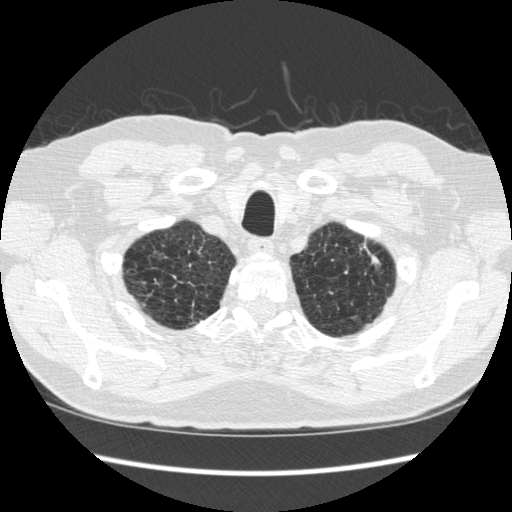
Chest CT (low-dose screening protocol), one axial image. Second screening round (one year after baseline). Lung window (W 1500 / L -600 HU). 1.25 mm slice thickness. Standard (soft-tissue) reconstruction kernel (STANDARD). 120 kVp. 512 × 512 image matrix, field of view 348 × 348 mm. Male participant, aged 70 years at enrolment. Former smoker at enrolment.
• Expert-annotated lung lesion, bounding box <325,233,388,302> (left, top, right, bottom; pixels).
• The screening reader recorded 5 non-calcified nodules or masses ≥4 mm on this exam (right lower lobe, right lower lobe, right lower lobe, left upper lobe, left lower lobe); which of them this box marks is not recorded.
• Official screen result: positive, change unspecified: nodule(s) >= 4 mm or enlarging nodule(s), mass(es), or other non-specific abnormalities suspicious for lung cancer.
• Participant outcome: lung cancer diagnosed 479 days after this screen (after the third annual screen) — squamous cell carcinoma, NOS, left upper lobe, moderately differentiated (G2), stage IA (AJCC 6th edition), 18 mm at pathology.